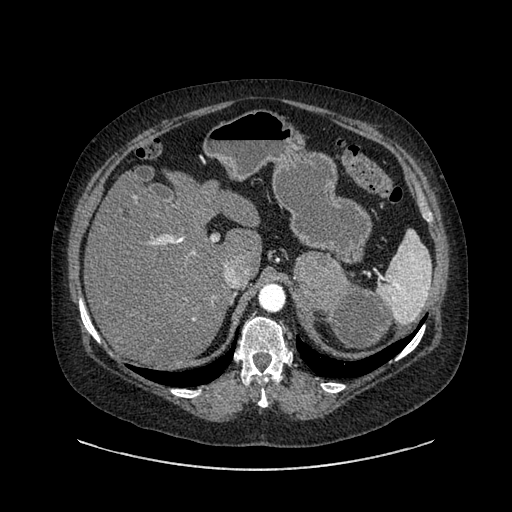
Contrast-enhanced abdominal CT, one axial slice. Position 613 of 769 along the scan axis. Reconstruction kernel SOFT. 120 kVp. Intravenous contrast given. Soft-tissue window (W 400 / L 40 HU). 512 × 512 image matrix. Patient: female, 61 years. From the clinical record (not read from this slice): diagnosis: adrenocortical carcinoma; tumour side: left adrenal; tumour size at pathology: 13 cm; Ki-67 index: 79 %; stage (as recorded): 2.
Outlined on this slice (semi-automatic segmentation, software-assisted and operator-edited):
- mass: box from (x=294, y=253) to (x=391, y=349) px